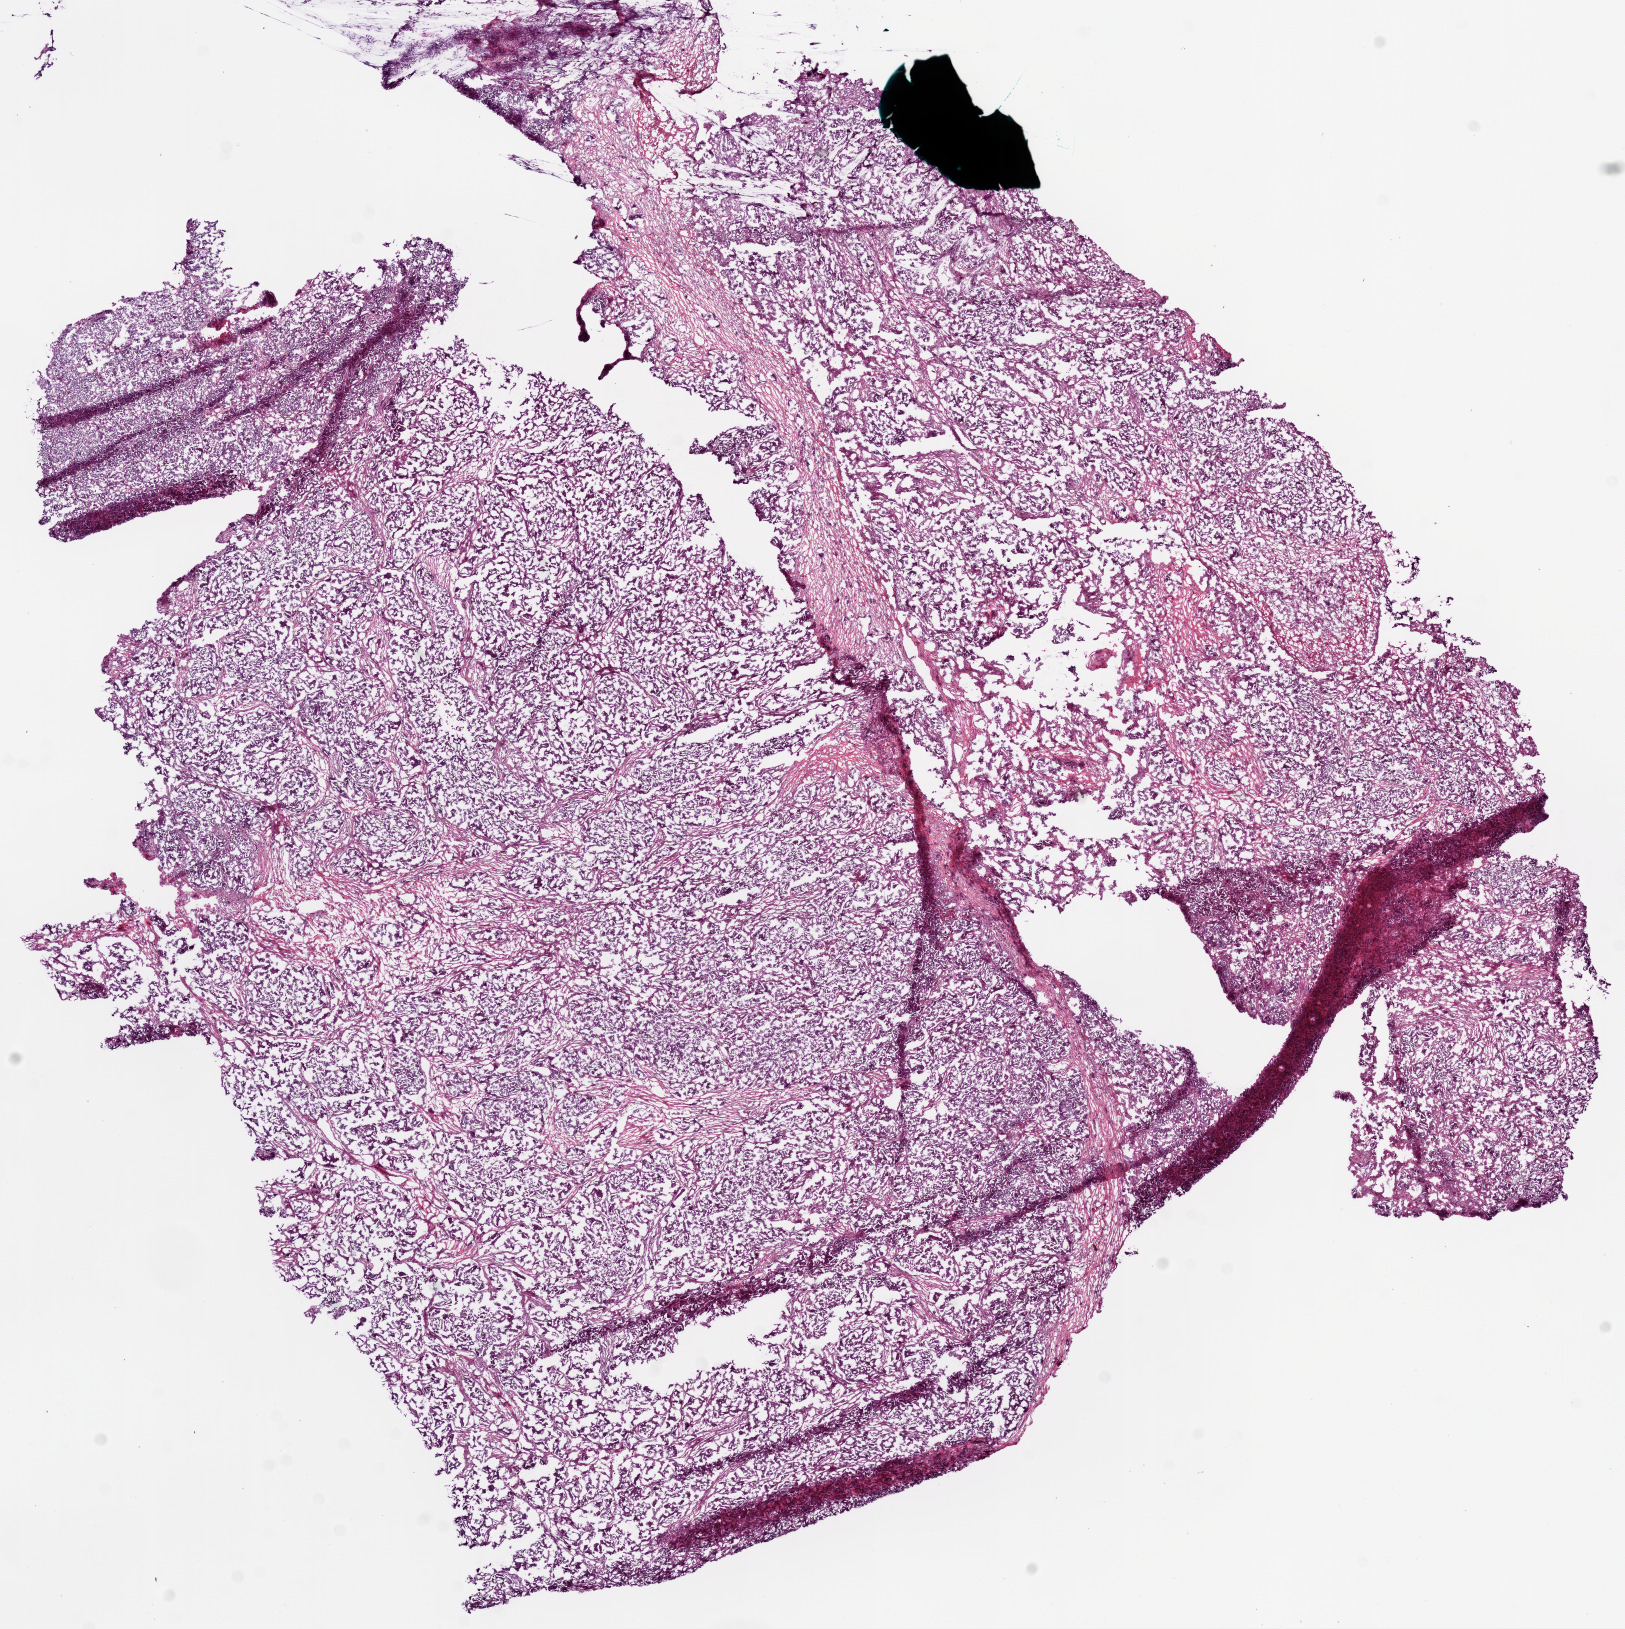
Hematoxylin and eosin (H&E) stained whole-slide image — shown as a low-resolution overview of the whole scanned area (about 13.0 x 13.1 mm), frozen section from the bottom of the tissue portion, primary tumour sample from the ovary. Patient: female, age at initial diagnosis 57 years. Histologic grade: G3 (poorly differentiated). Composition of this section per pathologist review: tumour cells 94%, tumour nuclei 95%, normal cells 0%, stromal cells 5%, necrosis 1%.
Histologic diagnosis: Serous cystadenocarcinoma, NOS. FIGO stage: IIIC.